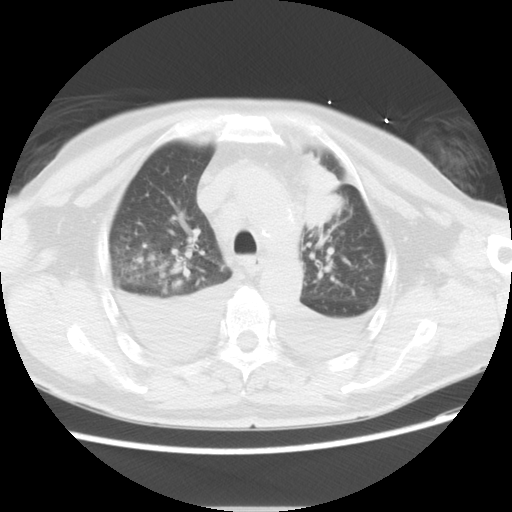
Chest CT, one axial slice; position 20 of 21 along the scan axis; 120 kVp; lung window (W 1500 / L -600 HU); 512 × 512 image matrix. Patient: male, 66 years. Case-level facts recorded for this patient, not image findings: clinical TNM (as recorded): T1c N0 M0.
Annotated regions visible in this slice (rectangle marked by the reading radiologist):
- lung tumour (recorded histology: adenocarcinoma): bounding box [x1, y1, x2, y2] px = [295, 150, 342, 230]